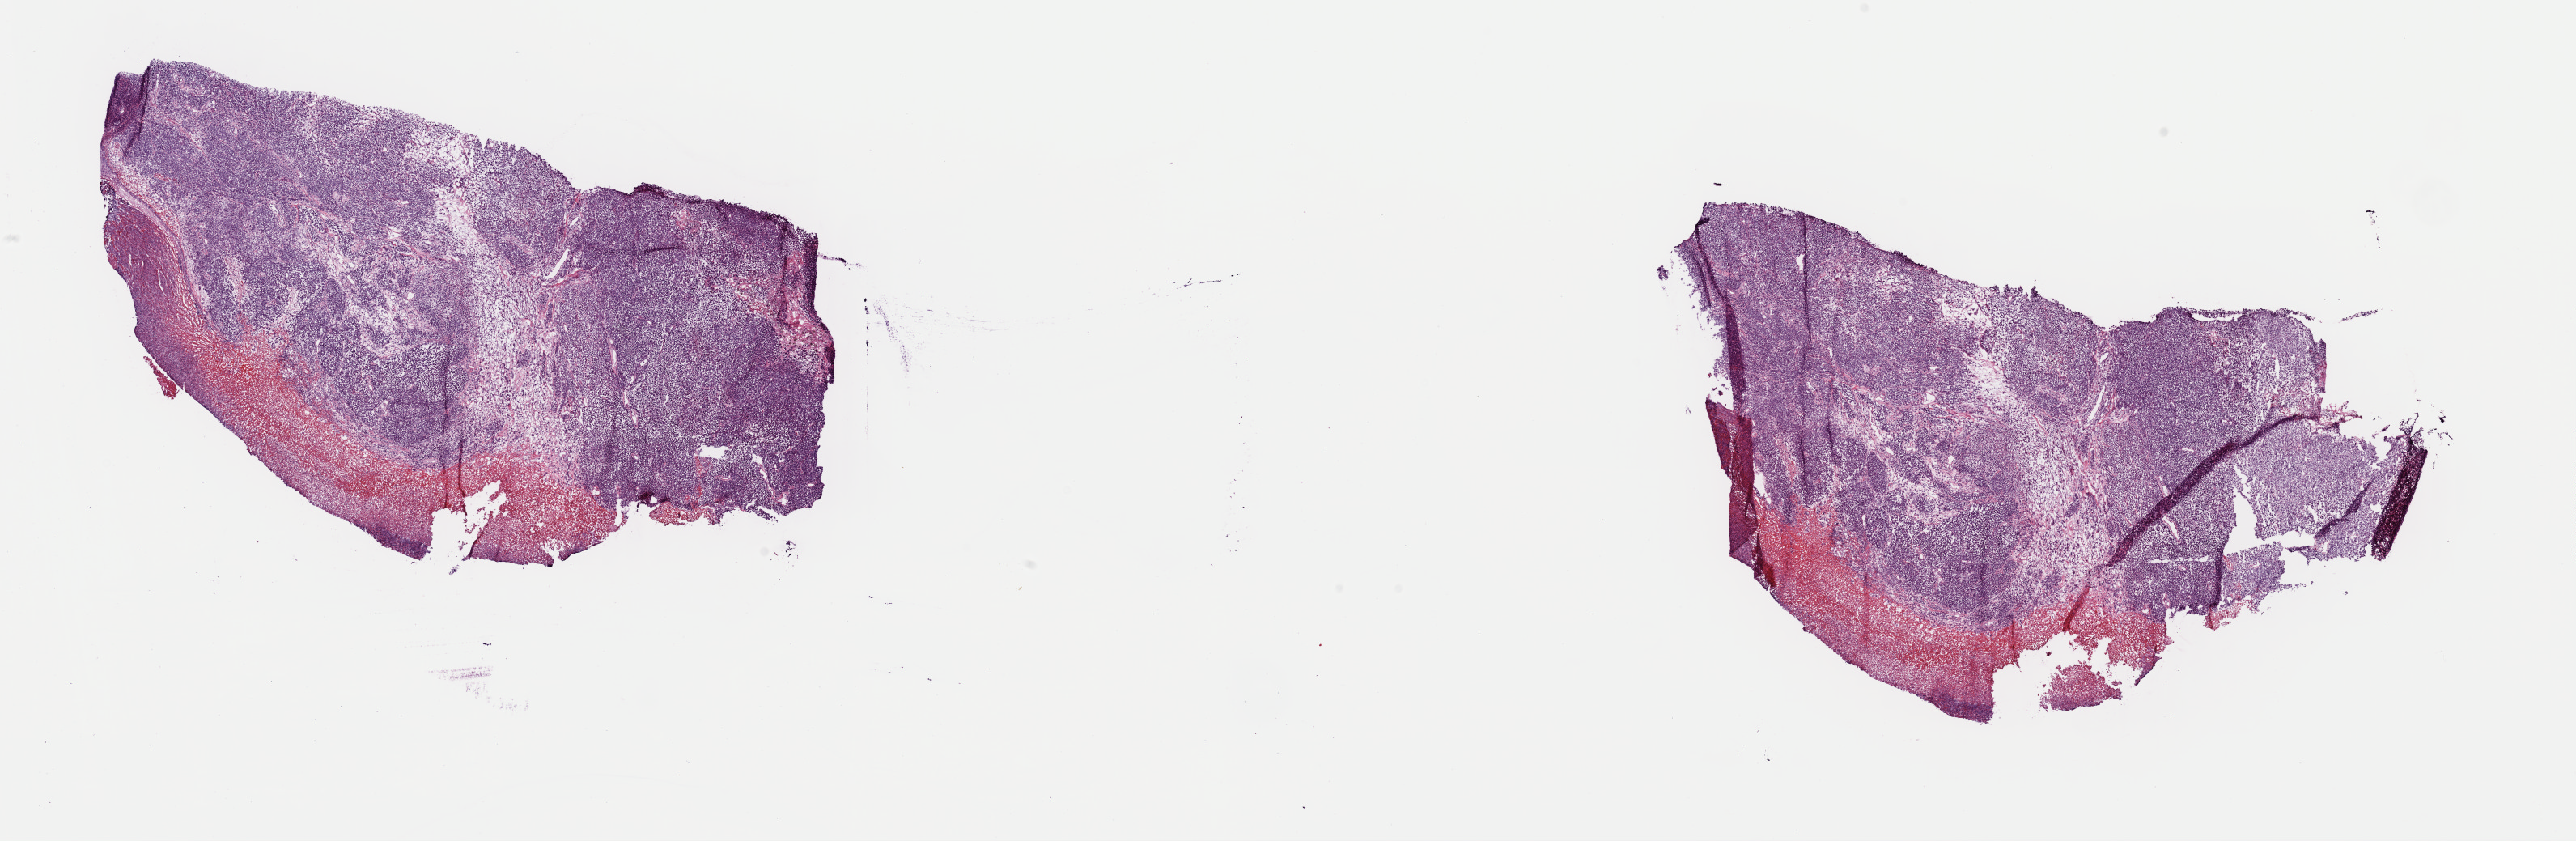
Whole-slide histology image, H&E, shown as a low-resolution overview of the whole scanned area (about 25.1 x 8.2 mm). Frozen section from the top of the tissue portion. Skin, primary tumour sample. Male patient. Slide review estimates, as recorded: tumour cells 80%, tumour nuclei 80%, normal cells 0%, stromal cells 10%, necrosis 10%. Inflammatory infiltration, as recorded: lymphocyte infiltration 0%, monocyte infiltration 0%, neutrophil infiltration 0%.
AJCC pathologic stage: IIC (7th edition). Pathologic diagnosis: Lentigo maligna melanoma.